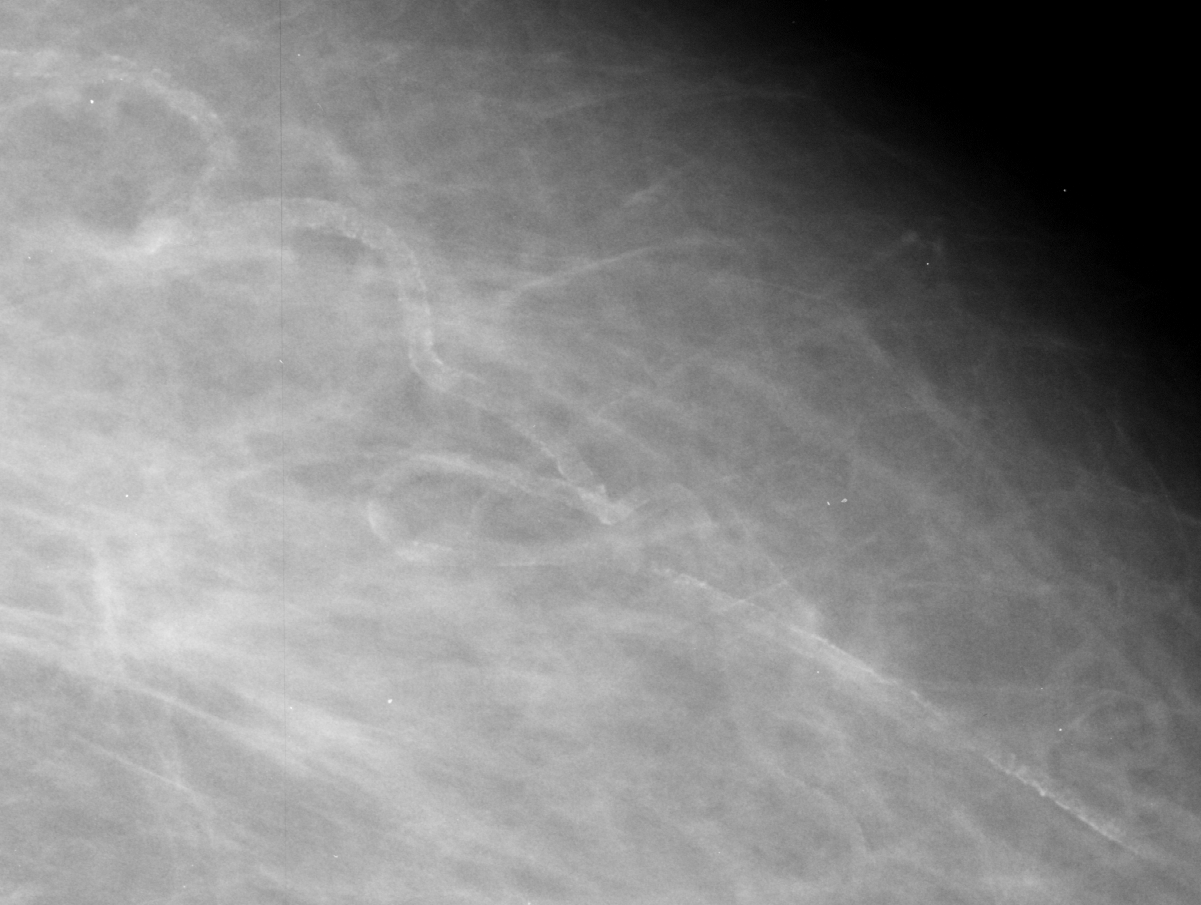
Crop from a digitized film mammogram around one marked abnormality, left breast, CC view.
Marked abnormality: calcifications, morphology vascular; BI-RADS assessment category 2; subtlety rating 3 on a 1 (subtle) to 5 (obvious) scale; benign; no additional work-up was recommended (benign without callback).